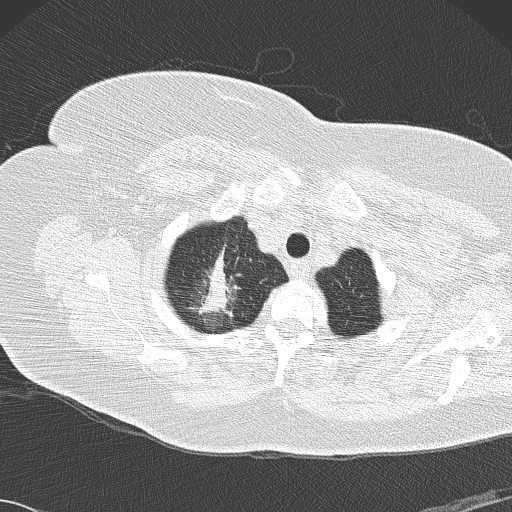
Low-dose screening chest CT, axial slice; second screening round (one year after baseline); lung window (W 1500 / L -600 HU); 2 mm slice thickness; 120 kVp; slice 18 of 146 in the series; 512 × 512 image matrix, field of view 350 × 350 mm. Female participant, aged 72 years at enrolment. Former smoker at enrolment.
• Expert reader's lesion annotation, bounding box [x1, y1, x2, y2] px = [183, 246, 258, 327].
• The screening reader recorded 4 non-calcified nodules or masses ≥4 mm on this exam (right lower lobe, right lower lobe, right lower lobe, right upper lobe); which of them this box marks is not recorded.
• Official screen result: positive, other.
• Lung cancer was diagnosed 52 days after this screen: bronchiolo-alveolar adenocarcinoma, NOS, right upper lobe, stage IIIB (AJCC 6th edition), 45 mm at pathology.